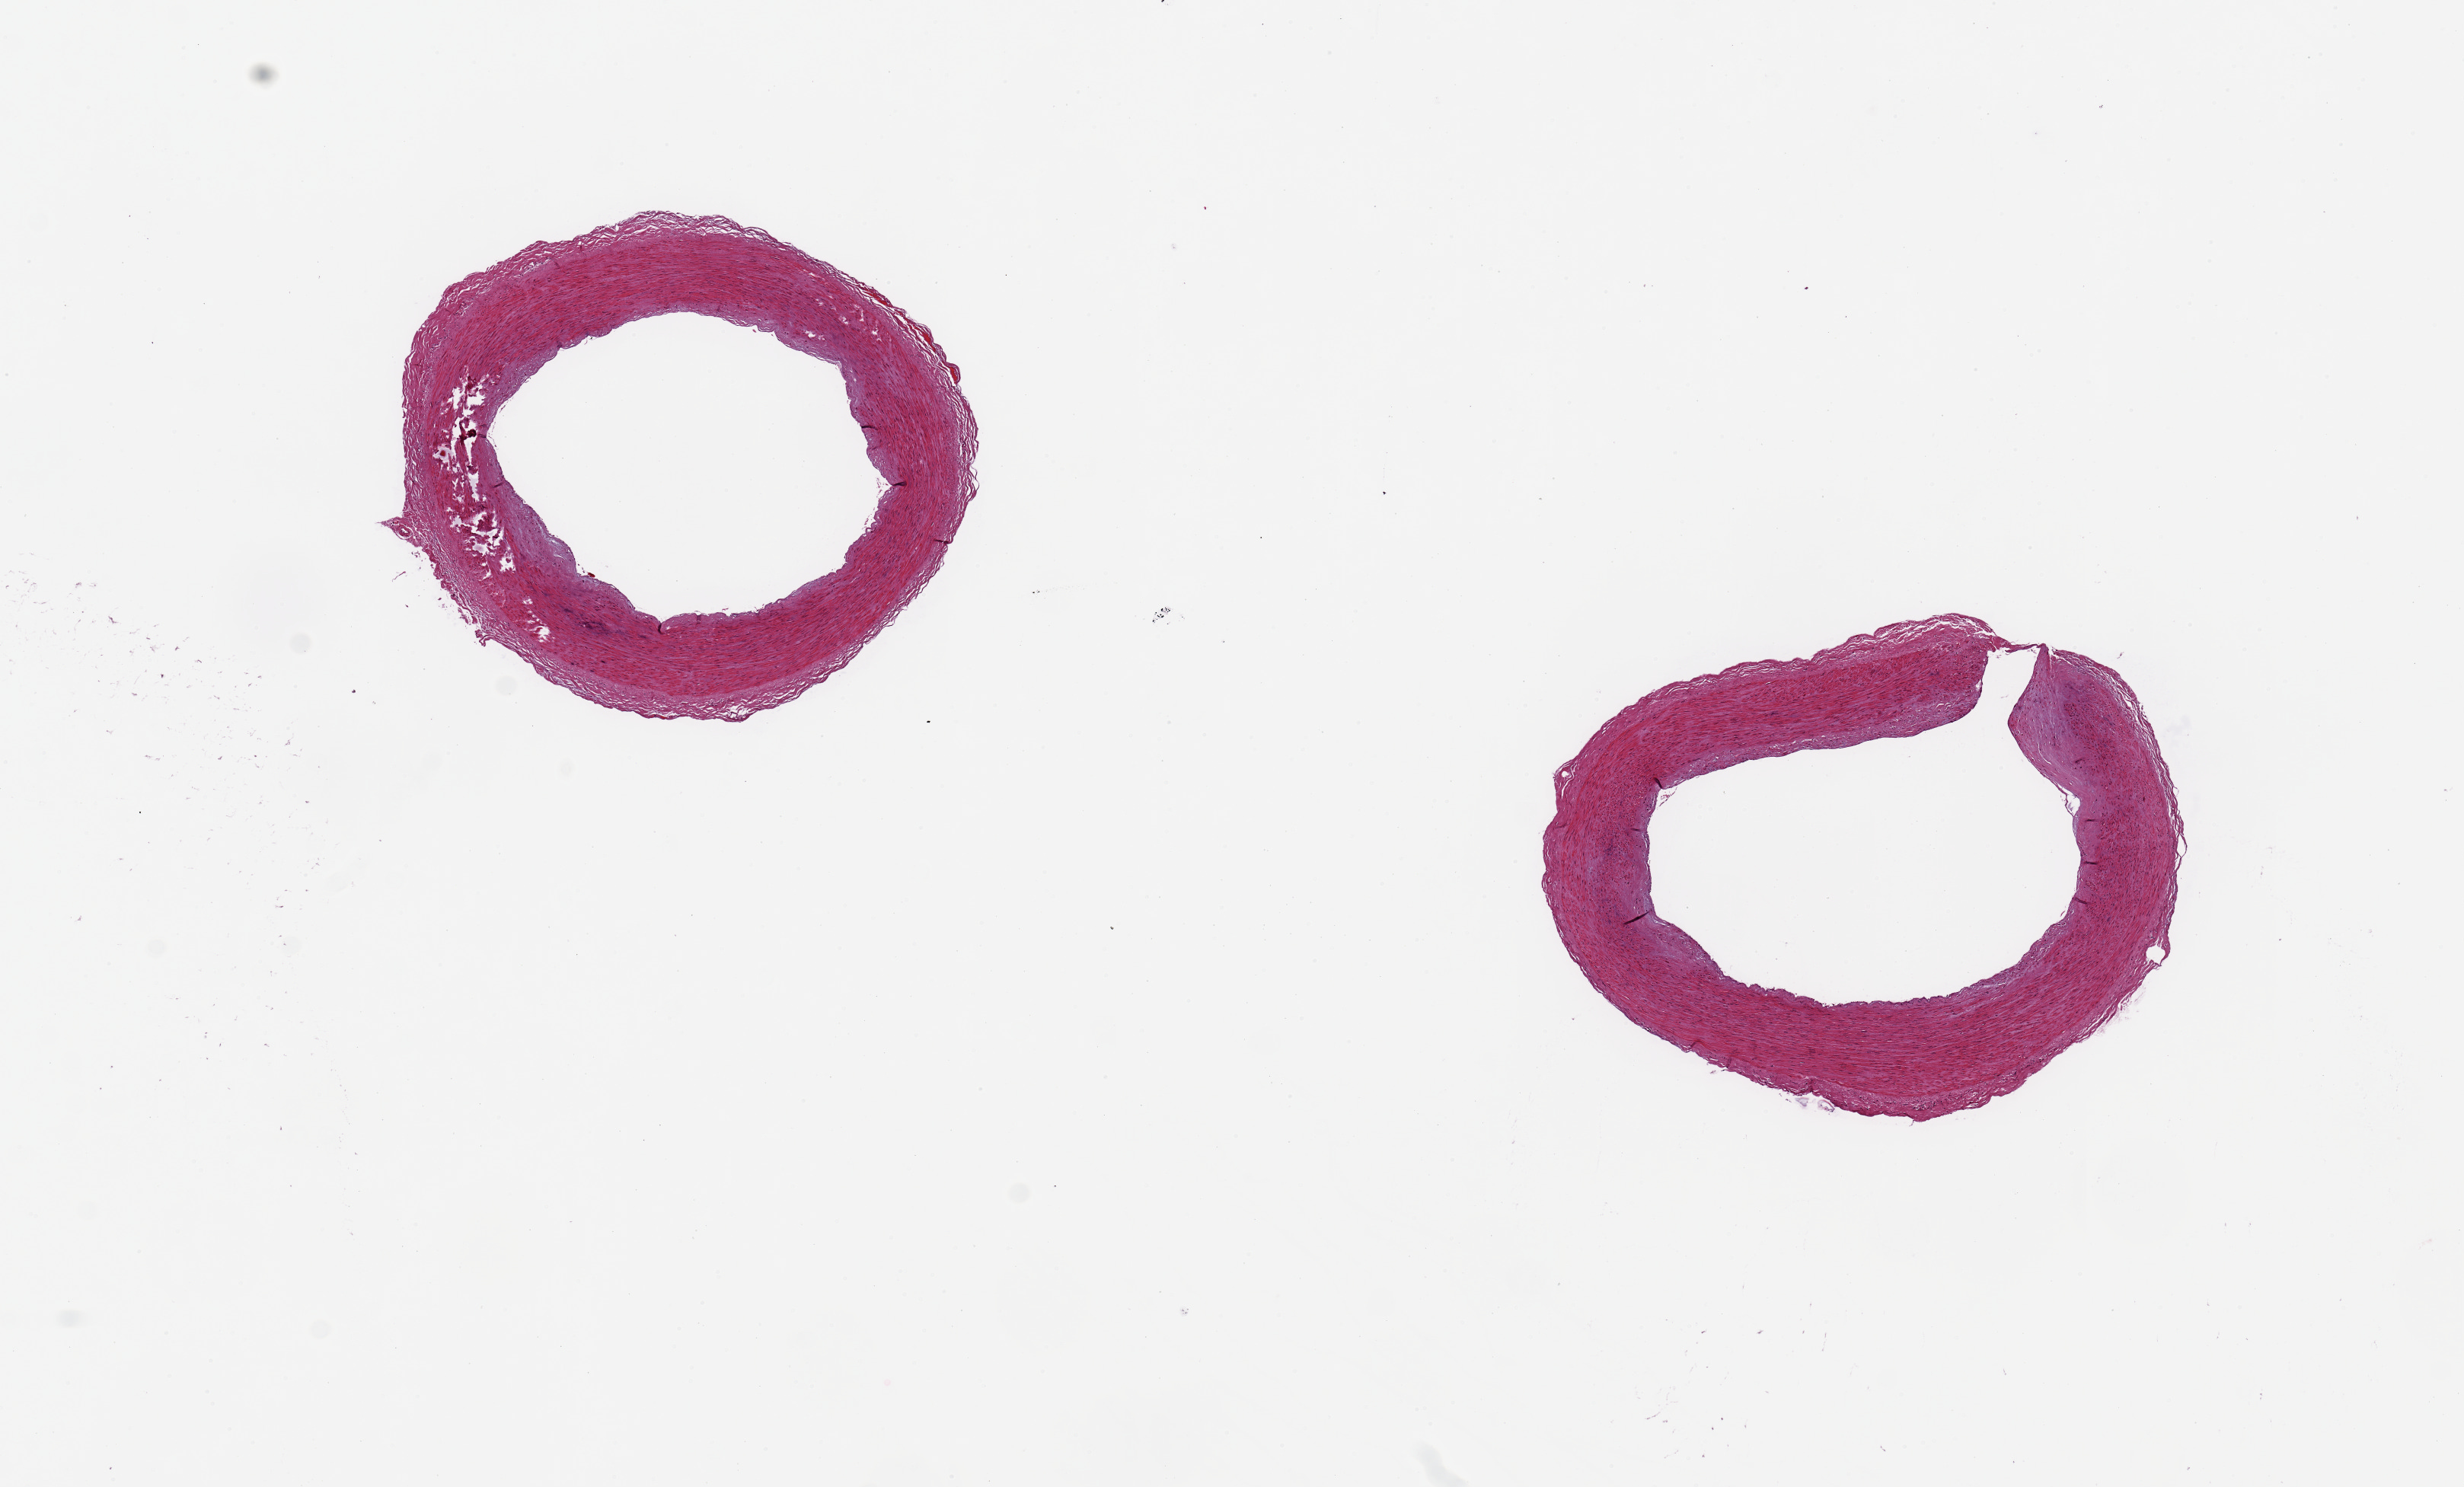
Hematoxylin and eosin (H&E) whole-slide image, brightfield, low-resolution overview of the scanned area, about 12.8 x 7.7 mm (slide scanned at 20x), PAXgene-fixed, paraffin-embedded tissue, section of tibial artery (target tissue), tissue donor sample. Donor sex: male.
Reviewer comment on this tissue sample: 2 pieces, 3x3 & 3x3mm; good clean specimens.